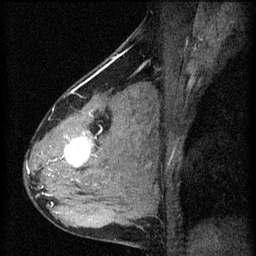
Breast MRI (dynamic contrast-enhanced), one sagittal slice. Slice 39 of 60 in the series (ordered by position). 3 images stored at this slice position (order not interpretable as contrast timing). 1.5 T. TE 4.2 ms, TR 8.2 ms. 2 mm slice thickness. 256 × 256 image matrix, field of view 180 × 180 mm. Female patient, age 37 years.
Annotated regions visible in this slice (semi-automatic segmentation, software-assisted and operator-edited):
- analysis volume of interest (the breast-tissue region the enhancement analysis was run in; not a lesion): bounding box [x1, y1, x2, y2] px = [44, 100, 119, 197]
- tumour enhancement mask (voxels above the 70 % enhancement threshold inside the analysis volume of interest): [50, 132, 98, 195]